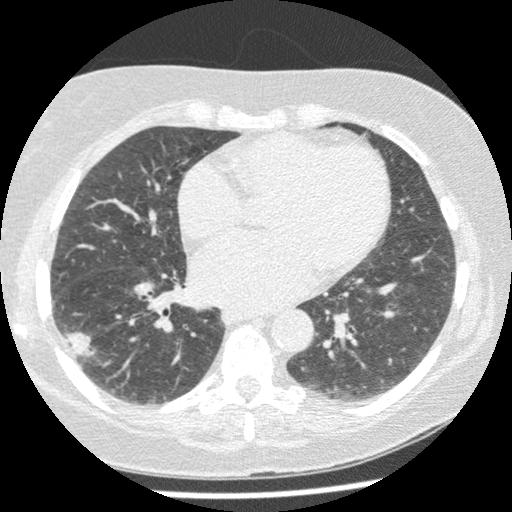
Low-dose screening chest CT, one axial slice. Slice 106 of 241 in the series (ordered by position). Reconstruction kernel STANDARD. 120 kVp. Lung window (W 1500 / L -600 HU). 1.25 mm slice thickness. 512 × 512 image matrix, field of view 305 × 305 mm.
Annotated regions visible in this slice (manually delineated by an expert):
- lesion 1 (tumor, lower lobe of right lung): bounding box [x1, y1, x2, y2] px = [64, 327, 96, 362]